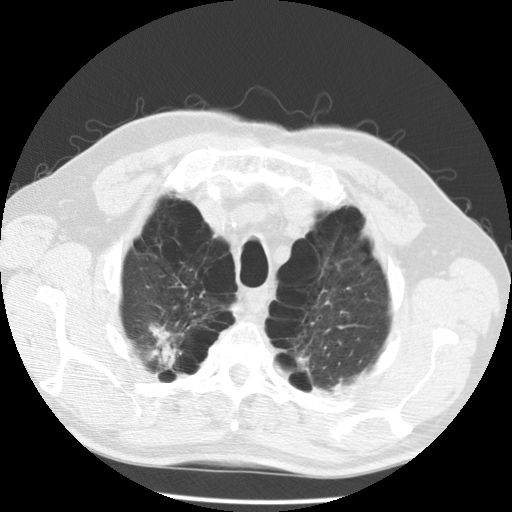
Chest CT (low-dose screening protocol), one axial image. Second annual screen. Lung window (W 1500 / L -600 HU). 2.5 mm slice thickness. Standard (soft-tissue) reconstruction kernel (STANDARD). Slice 26 of 167 in the series. Male, age 68 years at enrolment.
• Expert-annotated lung lesion, box from (x=125, y=306) to (x=199, y=381) px.
• The screening reader recorded 2 non-calcified nodules or masses ≥4 mm on this exam (lingula, left lower lobe); which of them this box marks is not recorded.
• Official screen result: positive, no significant change: stable abnormalities potentially related to lung cancer, unchanged since the prior screening exam.